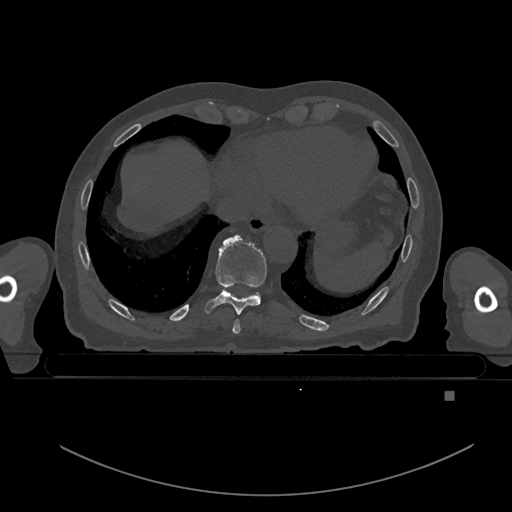
CT including the spine, one axial slice. Slice 142 of 969 in the series (ordered by position). Bone window (W 1800 / L 400 HU). 0.5 mm slice thickness. 512 × 512 image matrix, field of view 456 × 456 mm. Patient: male, 82 years. Case-level facts recorded for this patient, not image findings: primary cancer: prostate.
Annotated regions visible in this slice (semi-automatic segmentation, software-assisted and operator-edited):
- T8 vertebra: box from (x=232, y=319) to (x=241, y=334) px
- T9 vertebra: (x=204, y=235)–(x=267, y=315)